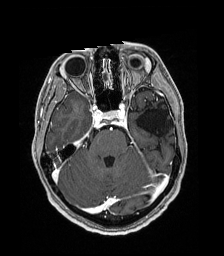
Brain MRI from a brain-tumour surgery series, one axial slice; position 123 of 192 along the scan axis; T1-weighted post-contrast; 1 mm slice thickness; 224 × 256 image matrix. Case-level facts recorded for this patient, not image findings: histopathology: Low grade glioma; IDH mutation: no; tumour location: Left Parieto-Occipital Intraventricular.
Annotated regions visible in this slice (manually delineated by an expert):
- previous resection cavity: bounding box [x1, y1, x2, y2] px = [136, 103, 172, 136]